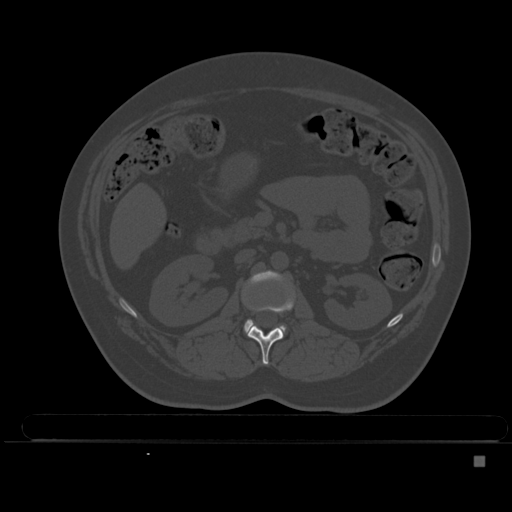
CT including the spine, one axial slice. Position 186 of 495 along the scan axis. Bone window (W 1800 / L 400 HU). 512 × 512 image matrix, field of view 404 × 404 mm. Female patient, age 33 years. Case-level facts recorded for this patient, not image findings: primary cancer: breast; vertebrae with lytic lesions (as recorded): T1.
Outlined on this slice (semi-automatically segmented with operator editing):
- L1 vertebra: bounding box [x1, y1, x2, y2] px = [247, 295, 295, 365]
- L2 vertebra: [244, 270, 286, 333]